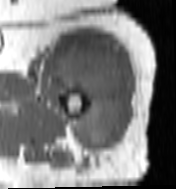
MRI of an extremity soft-tissue mass, one axial slice. Position 82 of 100 along the scan axis. MR volume resampled by the dataset authors to the PET/CT grid (not the native acquisition matrix). 176 × 189 image matrix, field of view 172 × 185 mm. Female patient. From the clinical record (not read from this slice): histological type: undifferentiated – high grade; grade: high; site of the primary tumour: left thigh.
Structures marked on this image (expert contour drawn on MRI and transferred to this co-registered scan by the dataset authors):
- gross tumour volume including surrounding oedema: box from (x=55, y=46) to (x=122, y=151) px
- gross tumour volume (mass): (x=57, y=50)–(x=122, y=151)